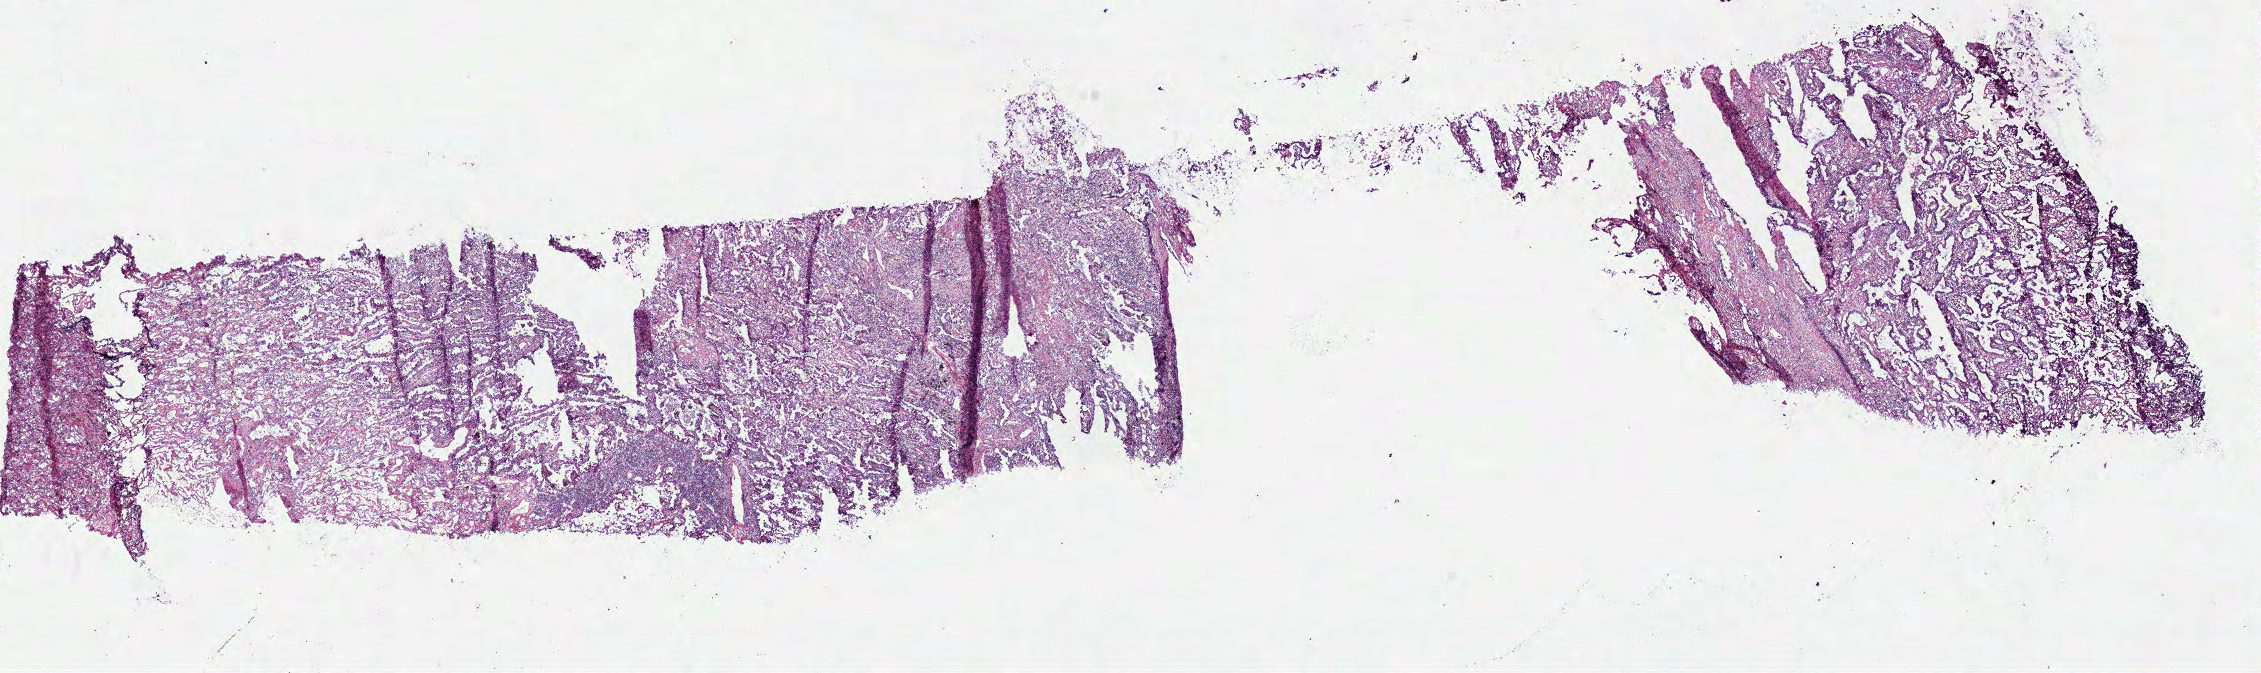
Whole-slide histology image, Hematoxylin and eosin (H&E) stained, whole scanned area (about 17.8 x 5.3 mm) shown as a low-resolution overview. Frozen section. Primary tumour sample from the lung. Female patient; age at initial diagnosis 64 years. Slide review estimates, as recorded: tumour cells 70%, tumour nuclei 75%, normal cells 15%, stromal cells 15%, necrosis 0%.
- histologic diagnosis: Adenocarcinoma with mixed subtypes (upper lobe, lung)
- AJCC pathologic stage: IIA (7th edition)